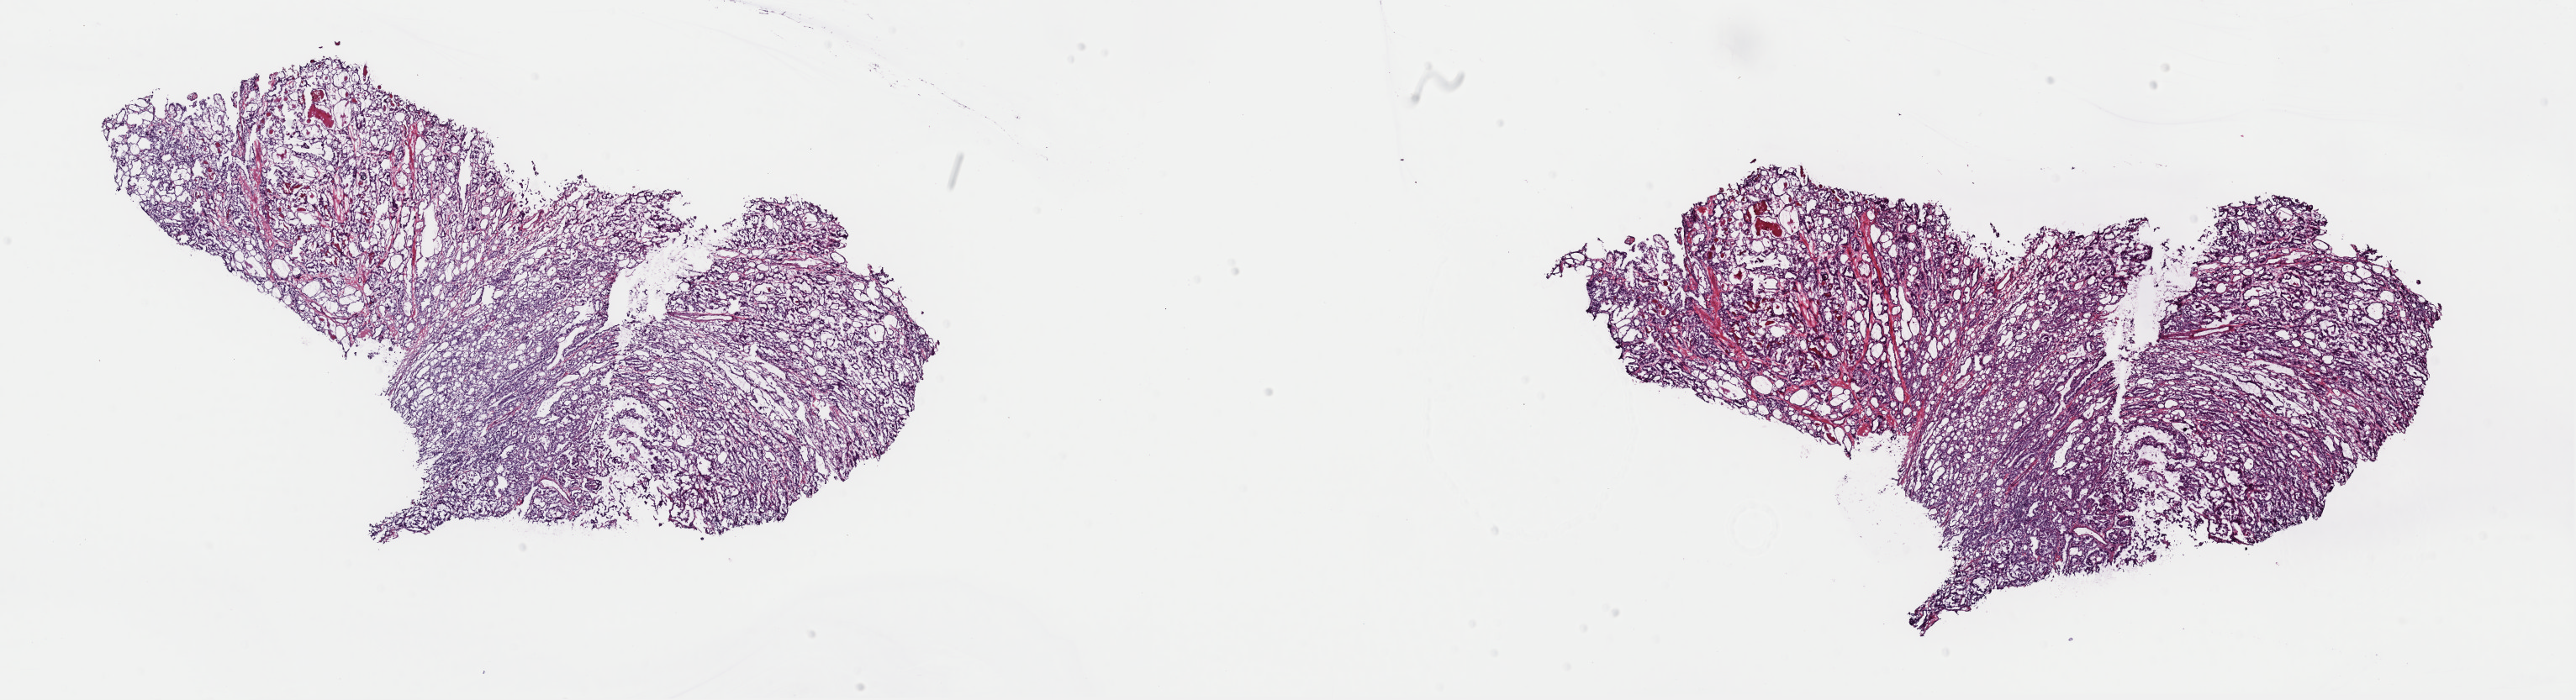
H&E-stained whole-slide image, a low-resolution overview of the entire scanned area, about 24.2 x 6.6 mm; frozen section from the top of the tissue portion; primary tumour sample from the thyroid. Patient: female, age at initial diagnosis 57 years. Composition of this section per pathologist review: tumour cells 85%, tumour nuclei 85%, normal cells 0%, stromal cells 15%, necrosis 0%. Infiltration values recorded for this section: lymphocyte infiltration 2%, monocyte infiltration 1%, neutrophil infiltration 1%.
* pathologic diagnosis: Papillary adenocarcinoma, NOS (thyroid gland)
* AJCC pathologic stage: II (7th edition)